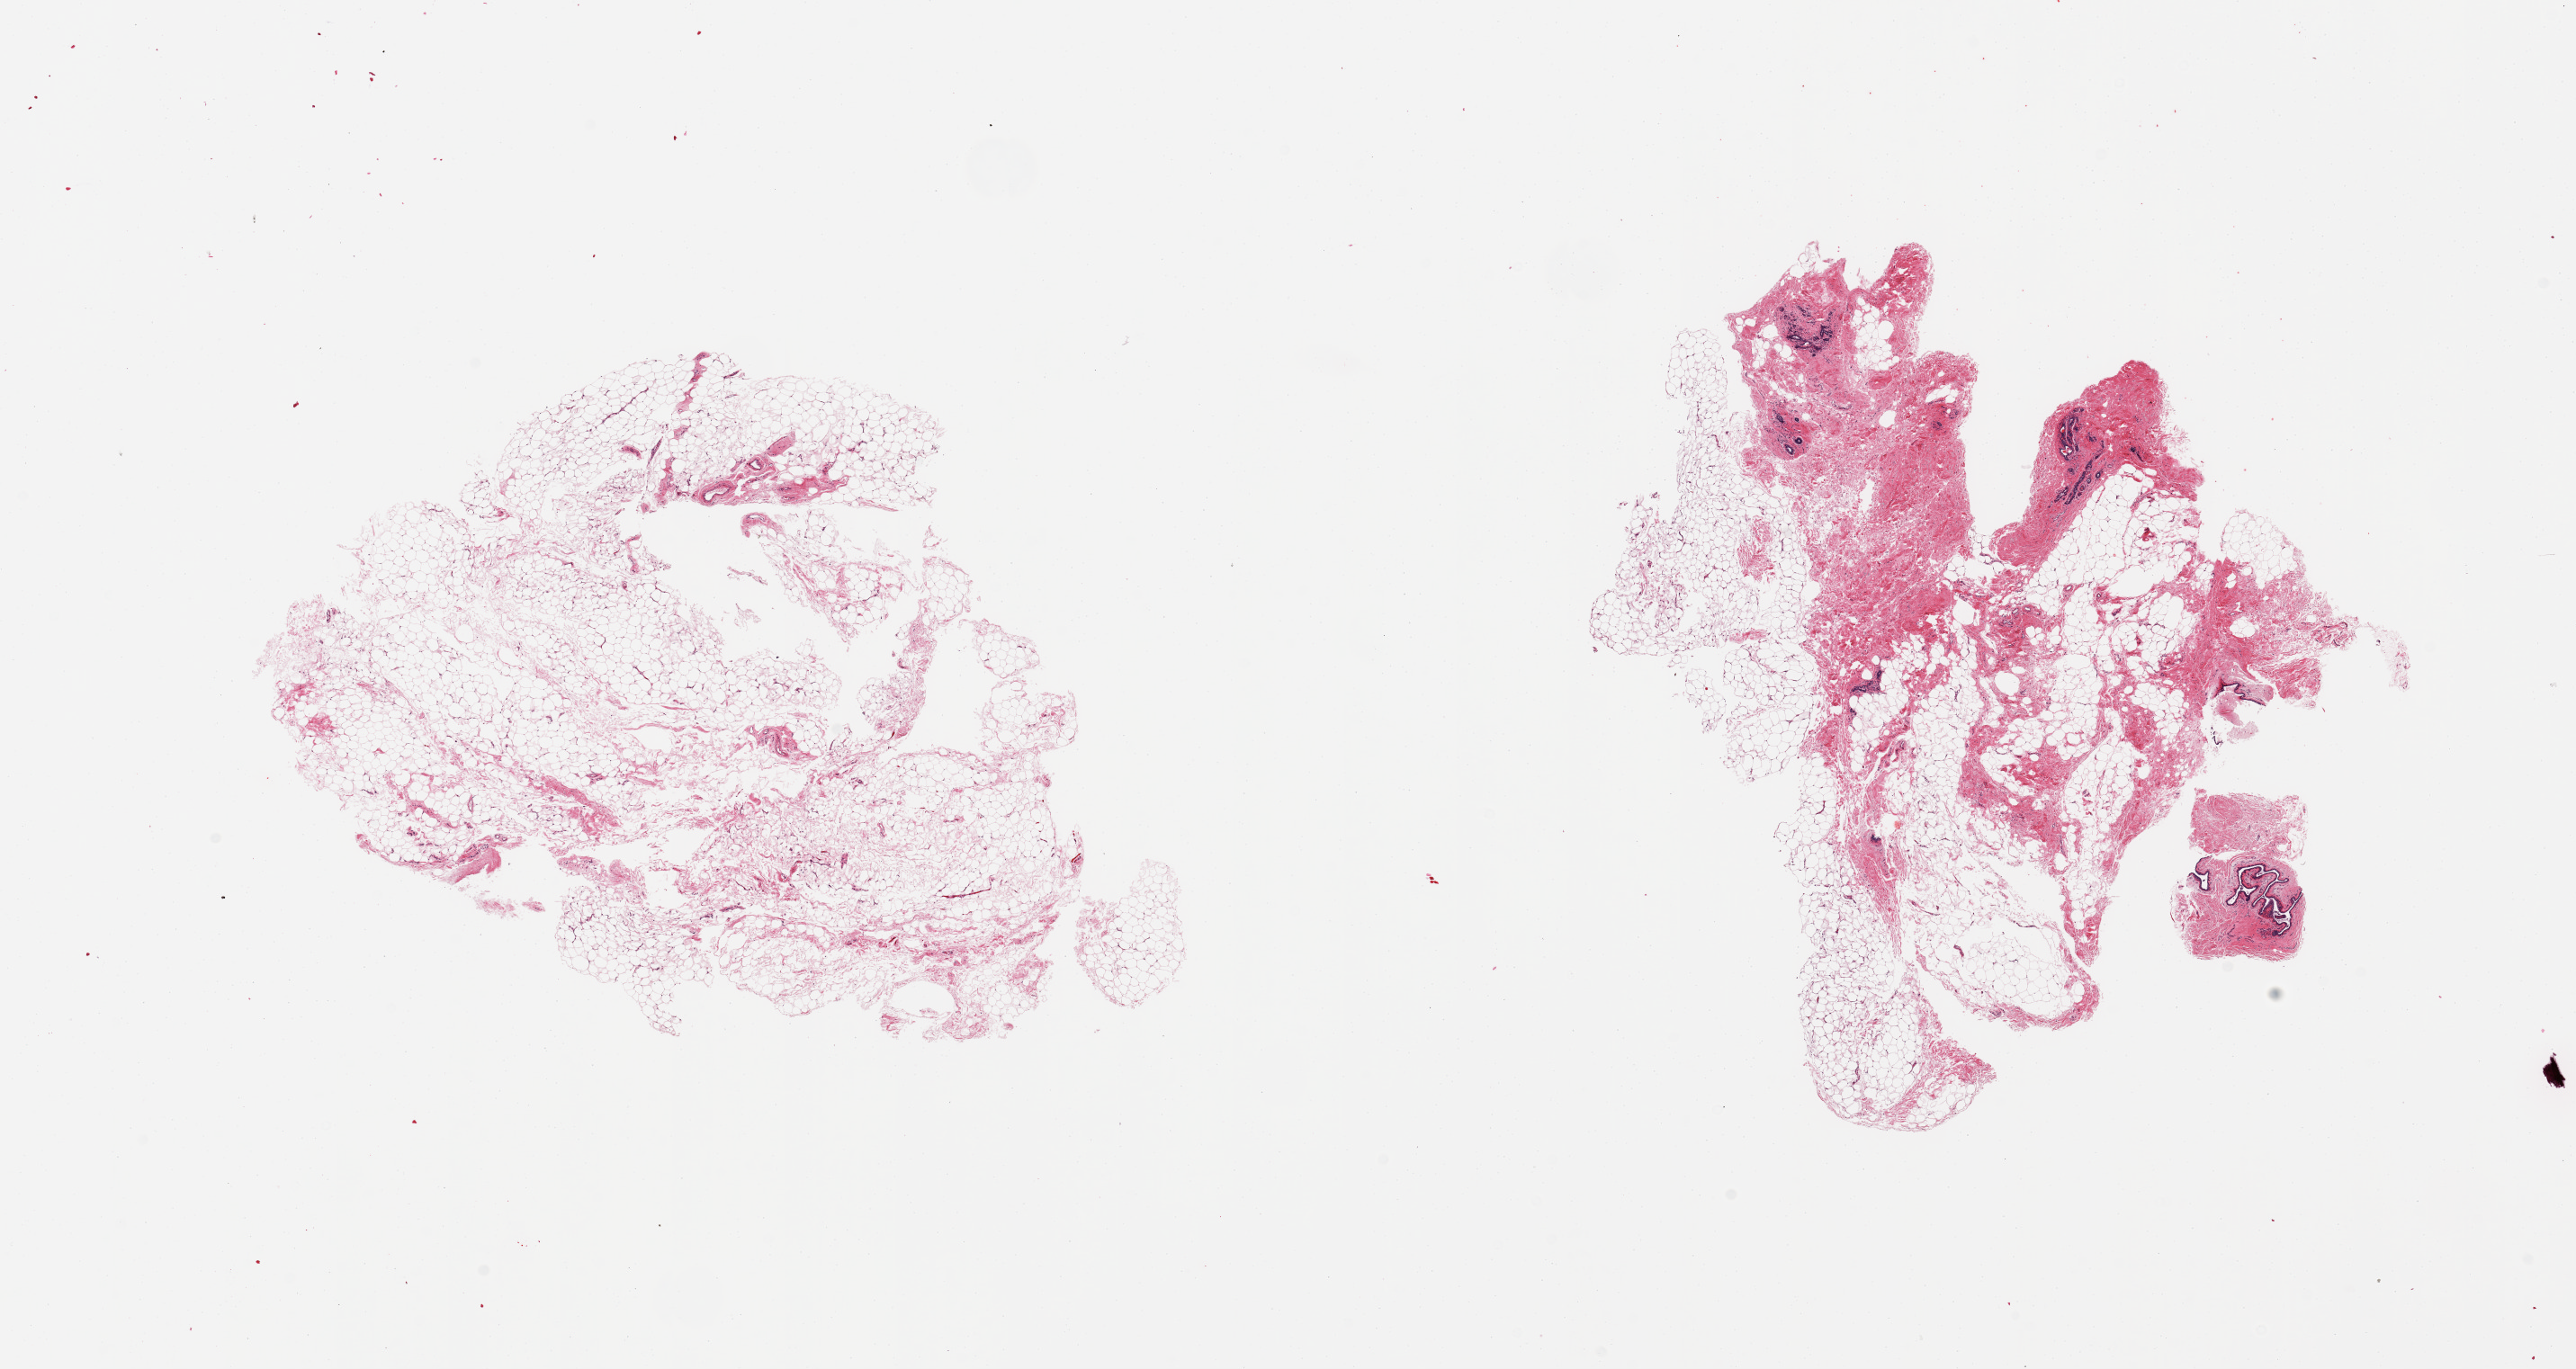
Digitized hematoxylin and eosin (H&E)-stained section, whole scanned area (about 22.6 x 12.0 mm) shown as a low-resolution overview, PAXgene-fixed paraffin-embedded (PFPE) section, target tissue: breast, donor tissue sample. Female donor.
- review note (as recorded): 2 pieces; scattered ducts and atrophic lobules; >50% fat